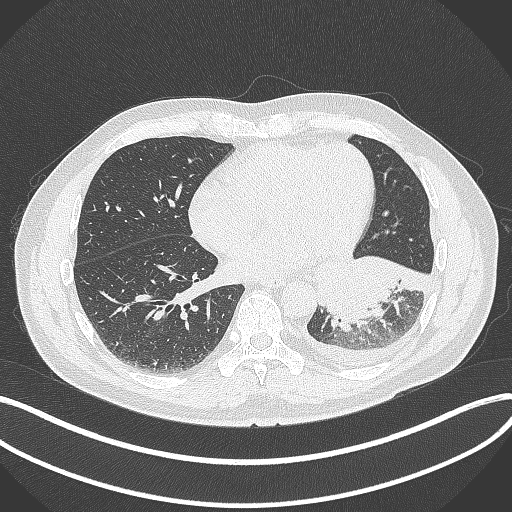
Chest CT, one axial slice; position 134 of 342 along the scan axis; lung window (W 1500 / L -600 HU); 512 × 512 image matrix. Patient: male, 58 years. Case-level facts recorded for this patient, not image findings: clinical TNM (as recorded): T3 N1 M1b.
Outlined on this slice (bounding box drawn by a radiologist):
- lung tumour (recorded histology: small cell carcinoma): bounding box (x1, y1, x2, y2) in pixels: (311, 248, 428, 332)